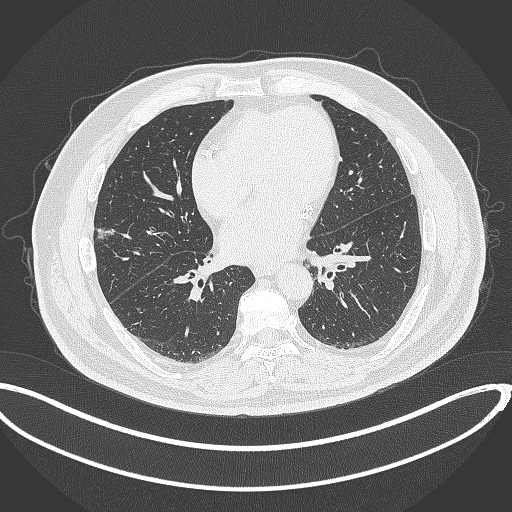
Chest CT, one axial slice; slice 142 of 340 in the series (ordered by position); reconstruction kernel B70f; 120 kVp; lung window (W 1500 / L -600 HU); 1 mm slice thickness; 512 × 512 image matrix, field of view 427 × 427 mm. Male patient, age 68 years. Case-level facts recorded for this patient, not image findings: clinical TNM (as recorded): T1c N0 M0.
Structures marked on this image (bounding box drawn by a radiologist):
- lung tumour (recorded histology: adenocarcinoma): box from (x=94, y=226) to (x=120, y=239) px